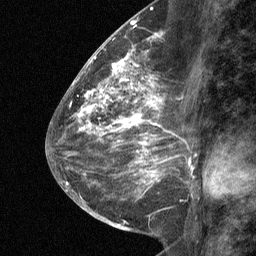
Breast MRI (dynamic contrast-enhanced), one sagittal slice. Dynamic contrast-enhanced study with each time point stored as its own series, time point 2 of 3 at this slice position (early post-contrast, ordered by acquisition time). 1.5 T. TE 4.8 ms, TR 27 ms. 2 mm slice thickness. 256 × 256 image matrix, field of view 180 × 180 mm. Patient: female, 59 years. Case-level facts recorded for this patient, not image findings: setting: breast cancer imaged before/during neoadjuvant chemotherapy; receptor status: triple-negative.
Structures marked on this image (semi-automatically segmented with operator editing):
- analysis volume of interest (the breast-tissue region the enhancement analysis was run in; not a lesion): bounding box [x1, y1, x2, y2] px = [122, 58, 168, 109]
- tumour enhancement mask (voxels above the 90 % enhancement threshold inside the analysis volume of interest): [122, 58, 163, 109]